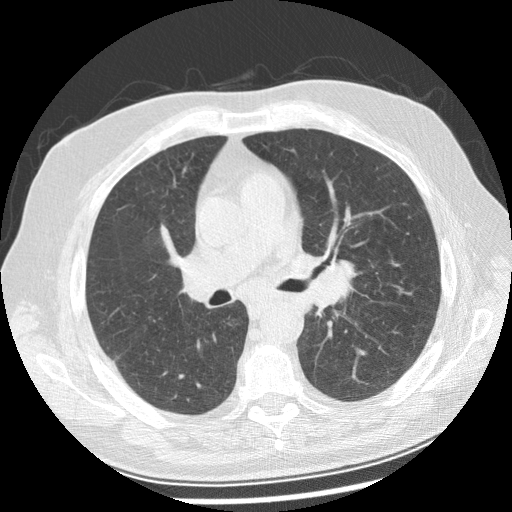
Low-dose screening chest CT, one axial slice. Position 145 of 250 along the scan axis. Lung window (W 1500 / L -600 HU). 2.5 mm slice thickness. 512 × 512 image matrix.
Outlined on this slice (expert manual segmentation):
- lesion 1 (tumor, left main bronchus): bounding box [x1, y1, x2, y2] px = [306, 260, 356, 309]